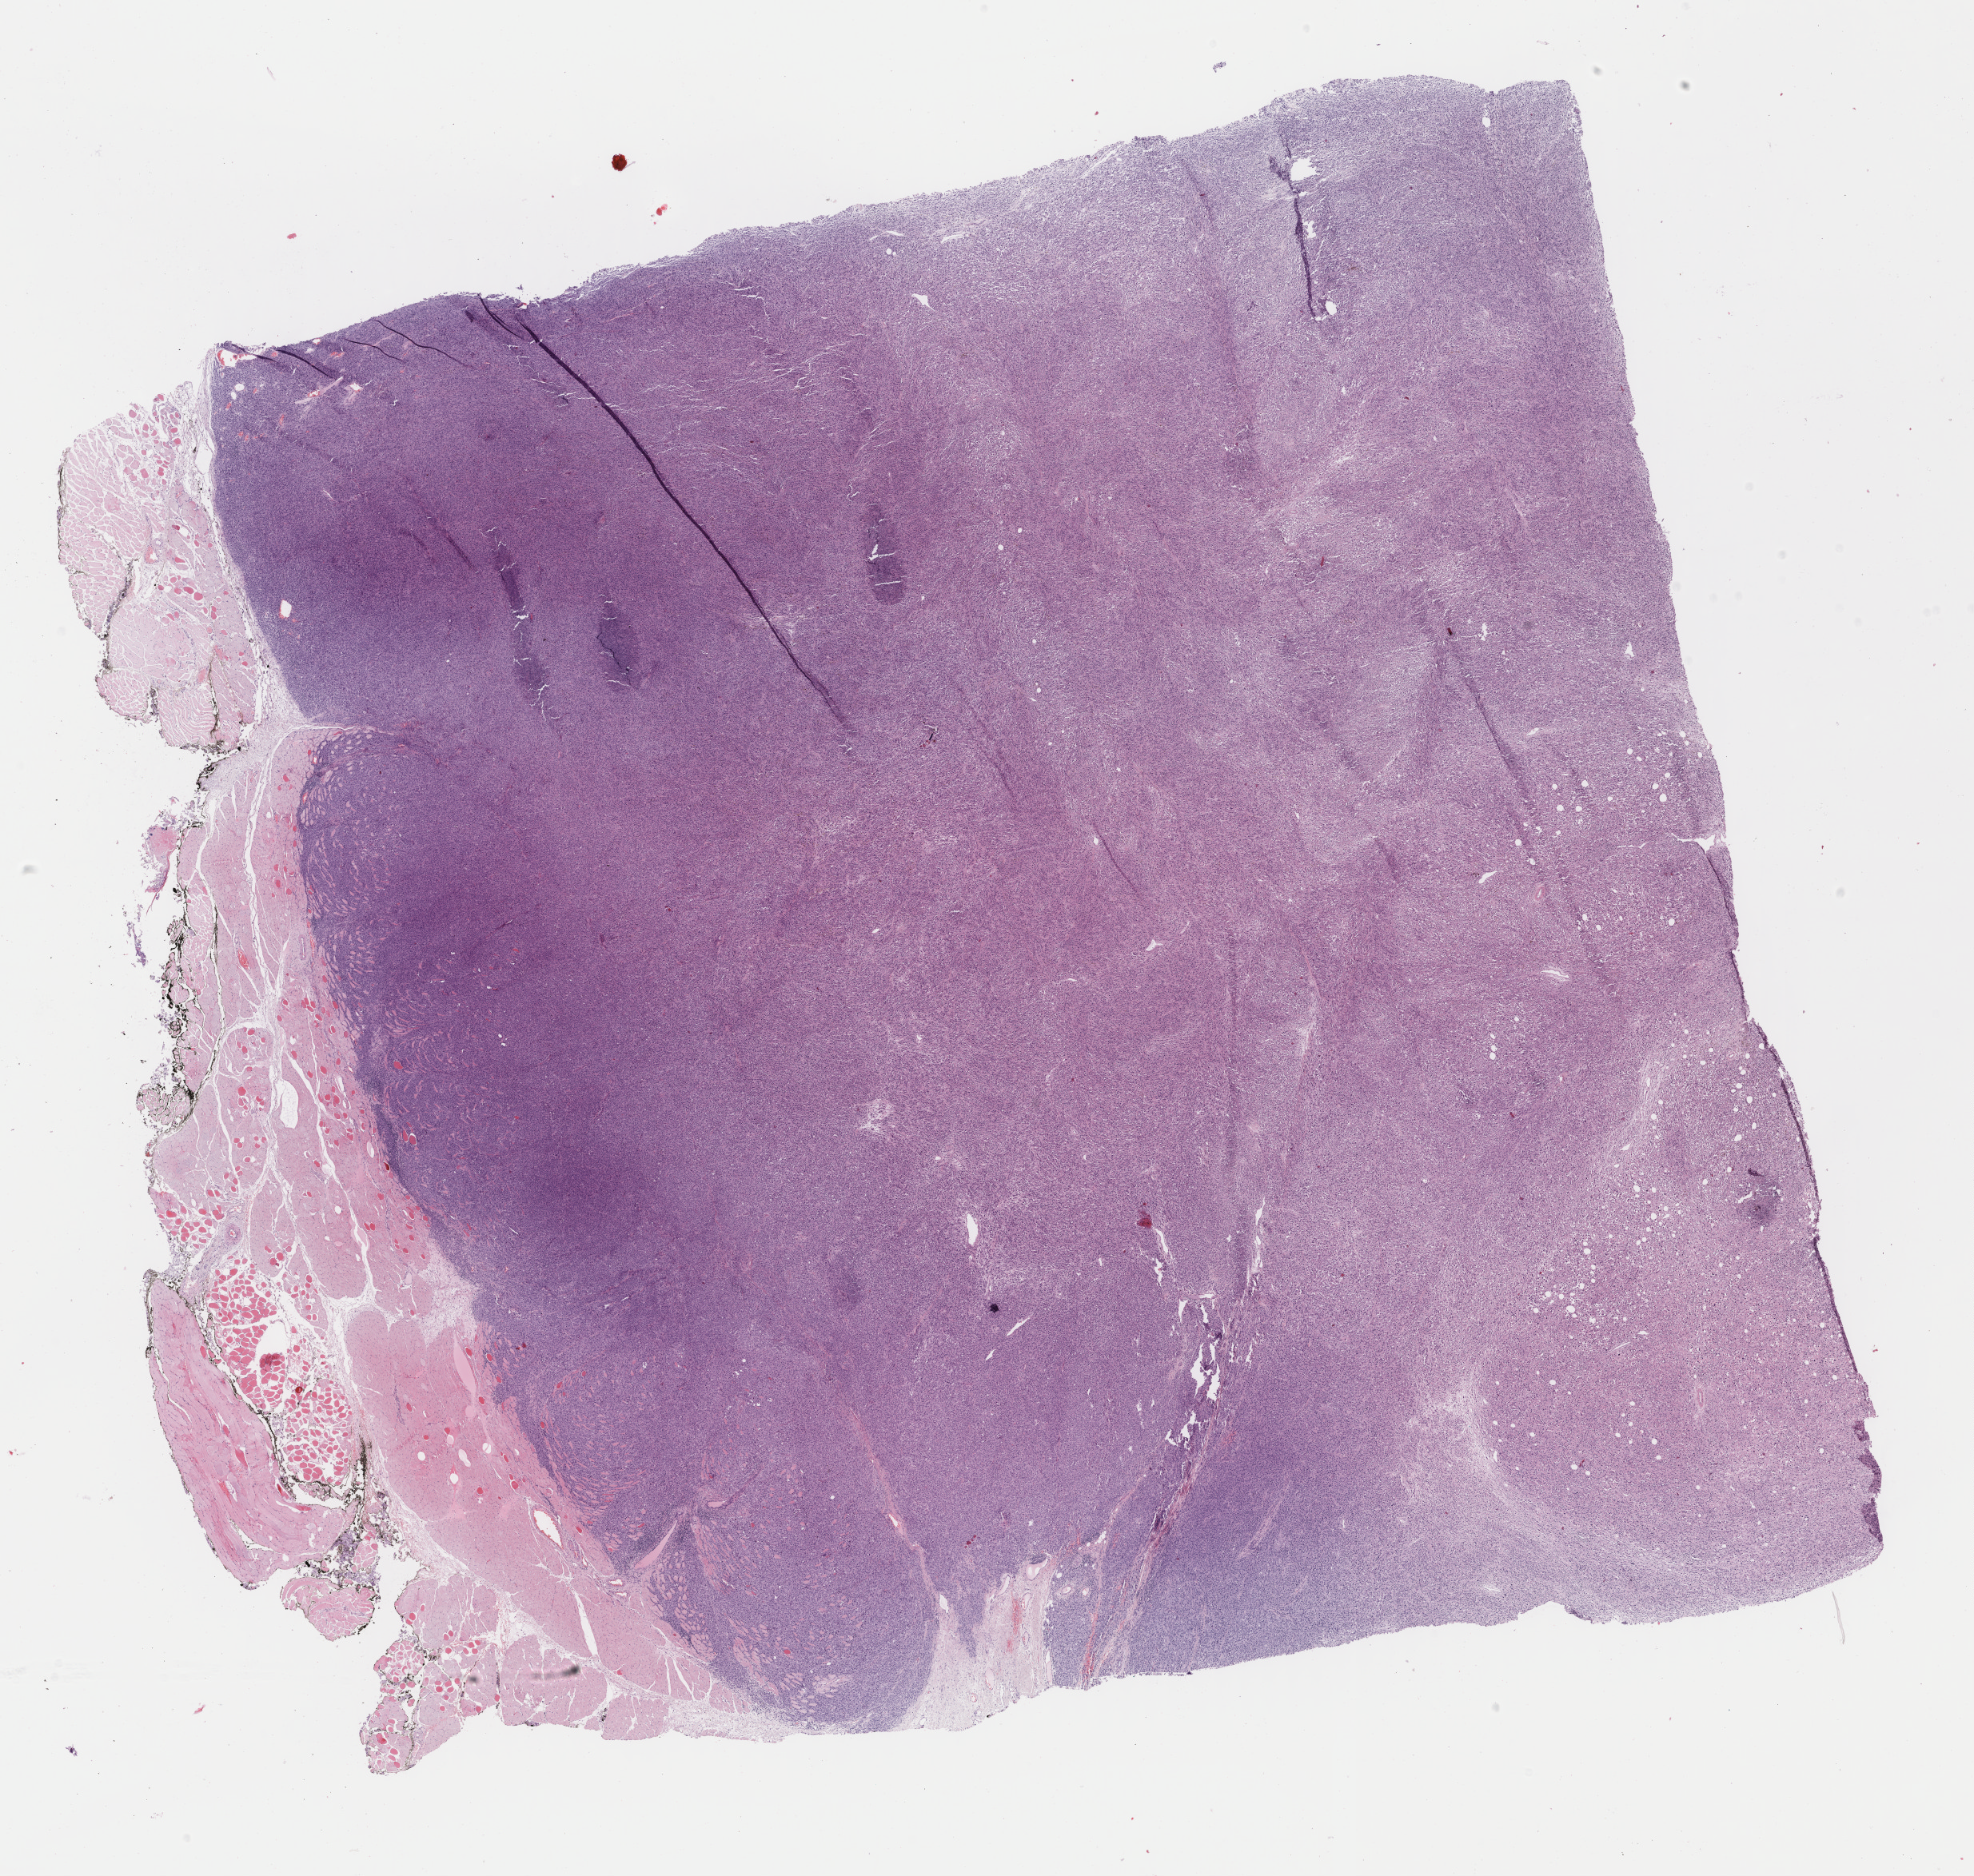
H&E whole-slide image, shown as a low-resolution overview of the whole scanned area (about 19.6 x 18.6 mm, acquisition: 40x scan). FFPE section. Skin, primary tumour sample. Female patient; age at initial diagnosis 73 years.
• histologic diagnosis: Nodular melanoma
• AJCC pathologic stage: IIIC (7th edition)